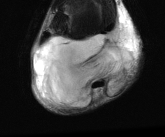
MRI of an extremity soft-tissue mass, one axial slice; position 17 of 81 along the scan axis; T2-weighted fat-saturated; MR volume resampled by the dataset authors to the PET/CT grid (not the native acquisition matrix); 165 × 137 image matrix, field of view 161 × 134 mm. Male patient. From the clinical record (not read from this slice): histological type: liposarcoma - round cell; grade: high; site of the primary tumour: right calf.
Annotated regions visible in this slice (expert contour drawn on MRI and transferred to this co-registered scan by the dataset authors):
- gross tumour volume (mass): box from (x=34, y=25) to (x=136, y=108) px